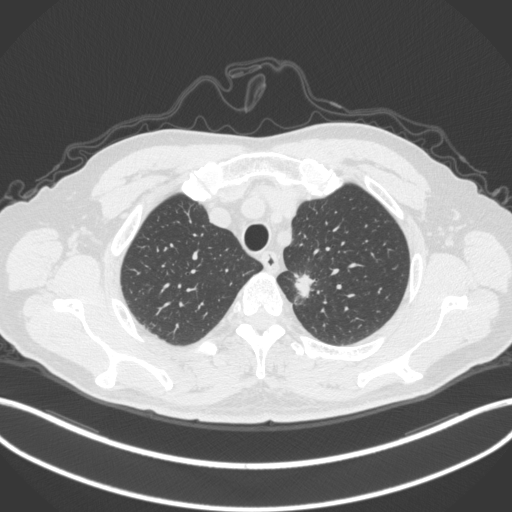
Chest CT, one axial slice. Position 311 of 382 along the scan axis. 120 kVp. Lung window (W 1500 / L -600 HU). 1 mm slice thickness. 512 × 512 image matrix, field of view 400 × 400 mm. Male patient, age 64 years. Case-level facts recorded for this patient, not image findings: clinical TNM (as recorded): T1c N0 M0.
Structures marked on this image (bounding box drawn by a radiologist):
- lung tumour (recorded histology: adenocarcinoma): bounding box [x1, y1, x2, y2] px = [292, 271, 320, 308]